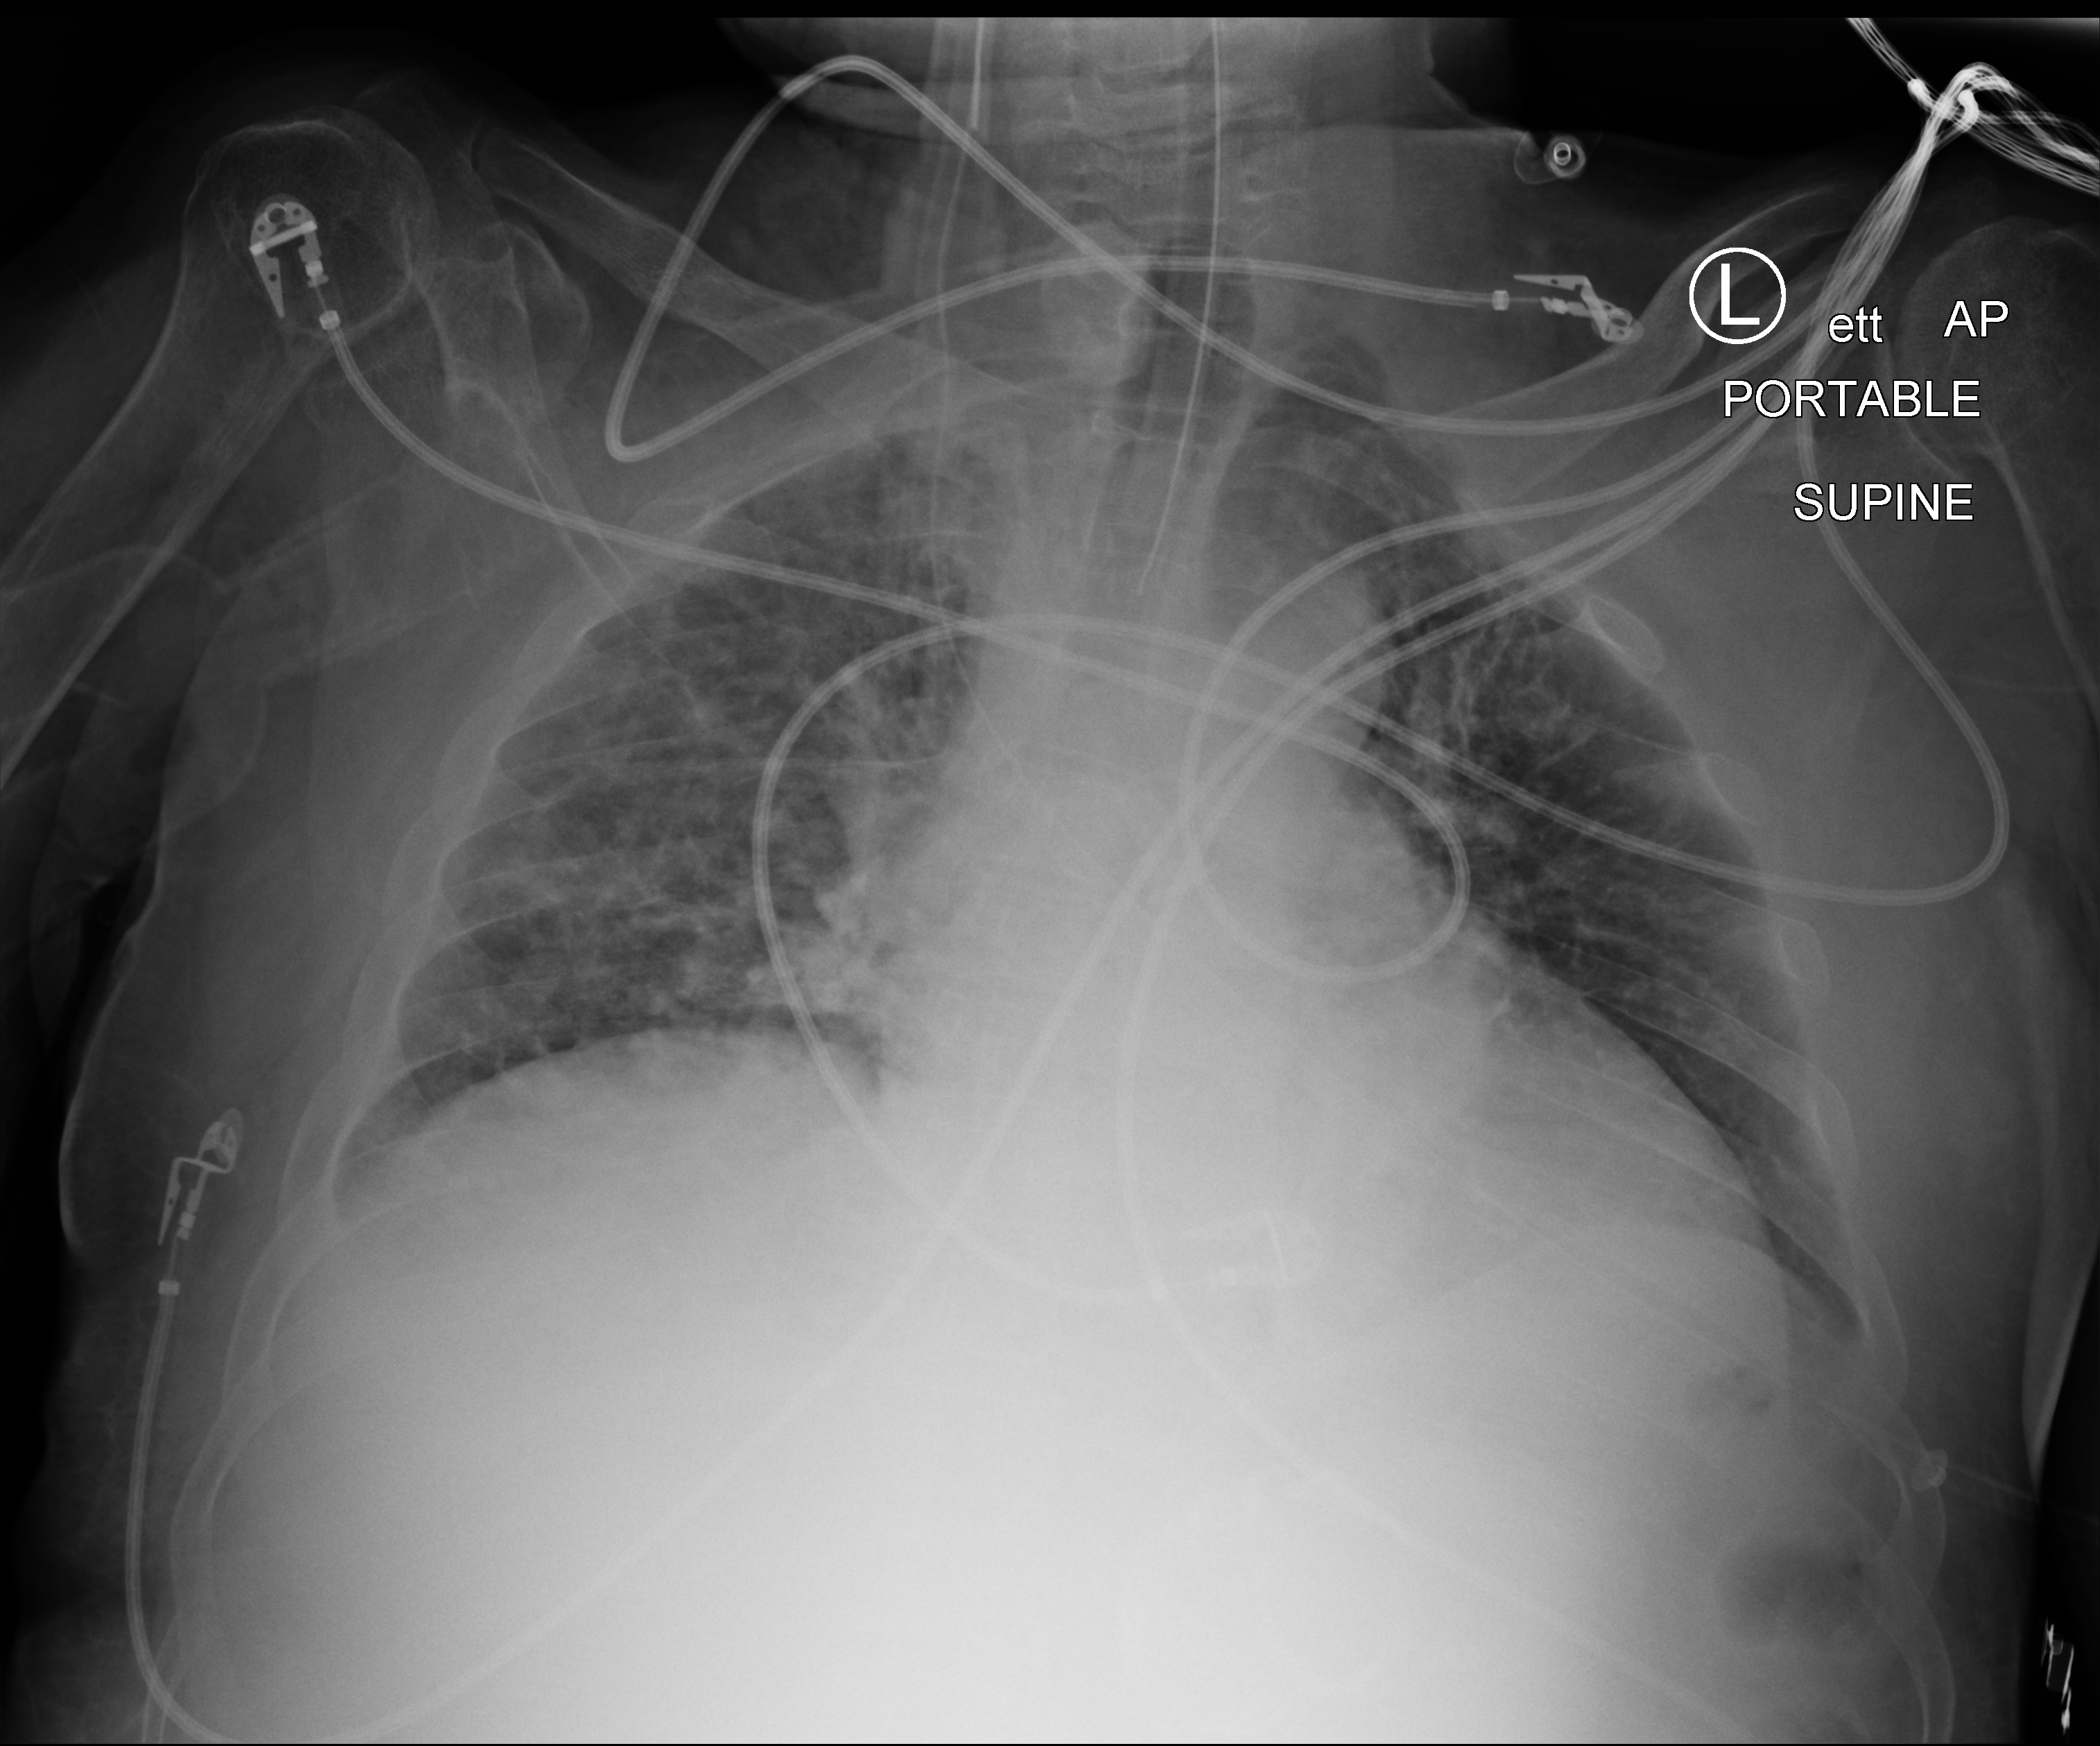
Bedside chest radiograph (computed radiography), anteroposterior (AP) projection. Male patient hospitalised with COVID-19, age 60–74 years.
From the hospital-stay record, not from the radiograph (when in the stay this image was taken is not recorded):
- mechanically ventilated during this hospital stay: yes
- admitted to intensive care during this hospital stay: yes